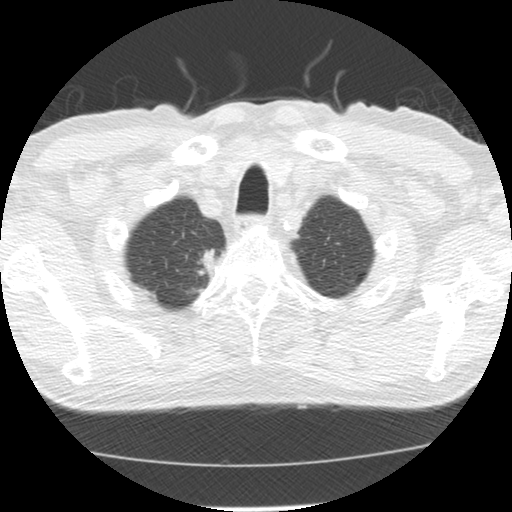
Chest CT (low-dose screening protocol), one axial image, baseline screening round, lung window (W 1500 / L -600 HU), slice 19 of 139 in the series. Male, age 64 years at enrolment. Former smoker at enrolment.
• Expert reader's lesion annotation, bounding box <182,243,224,283> (left, top, right, bottom; pixels).
• Reader record for this screening exam (exam-level; its link to the box is not recorded): non-calcified nodule or mass ≥4 mm, right upper lobe, 20 × 13 mm, spiculated (stellate) margins, soft tissue attenuation.
• Later outcome: lung cancer diagnosed 73 days after this screen — adenocarcinoma, NOS, right upper lobe, moderately differentiated (G2), stage IA (AJCC 6th edition), 17 mm at pathology.